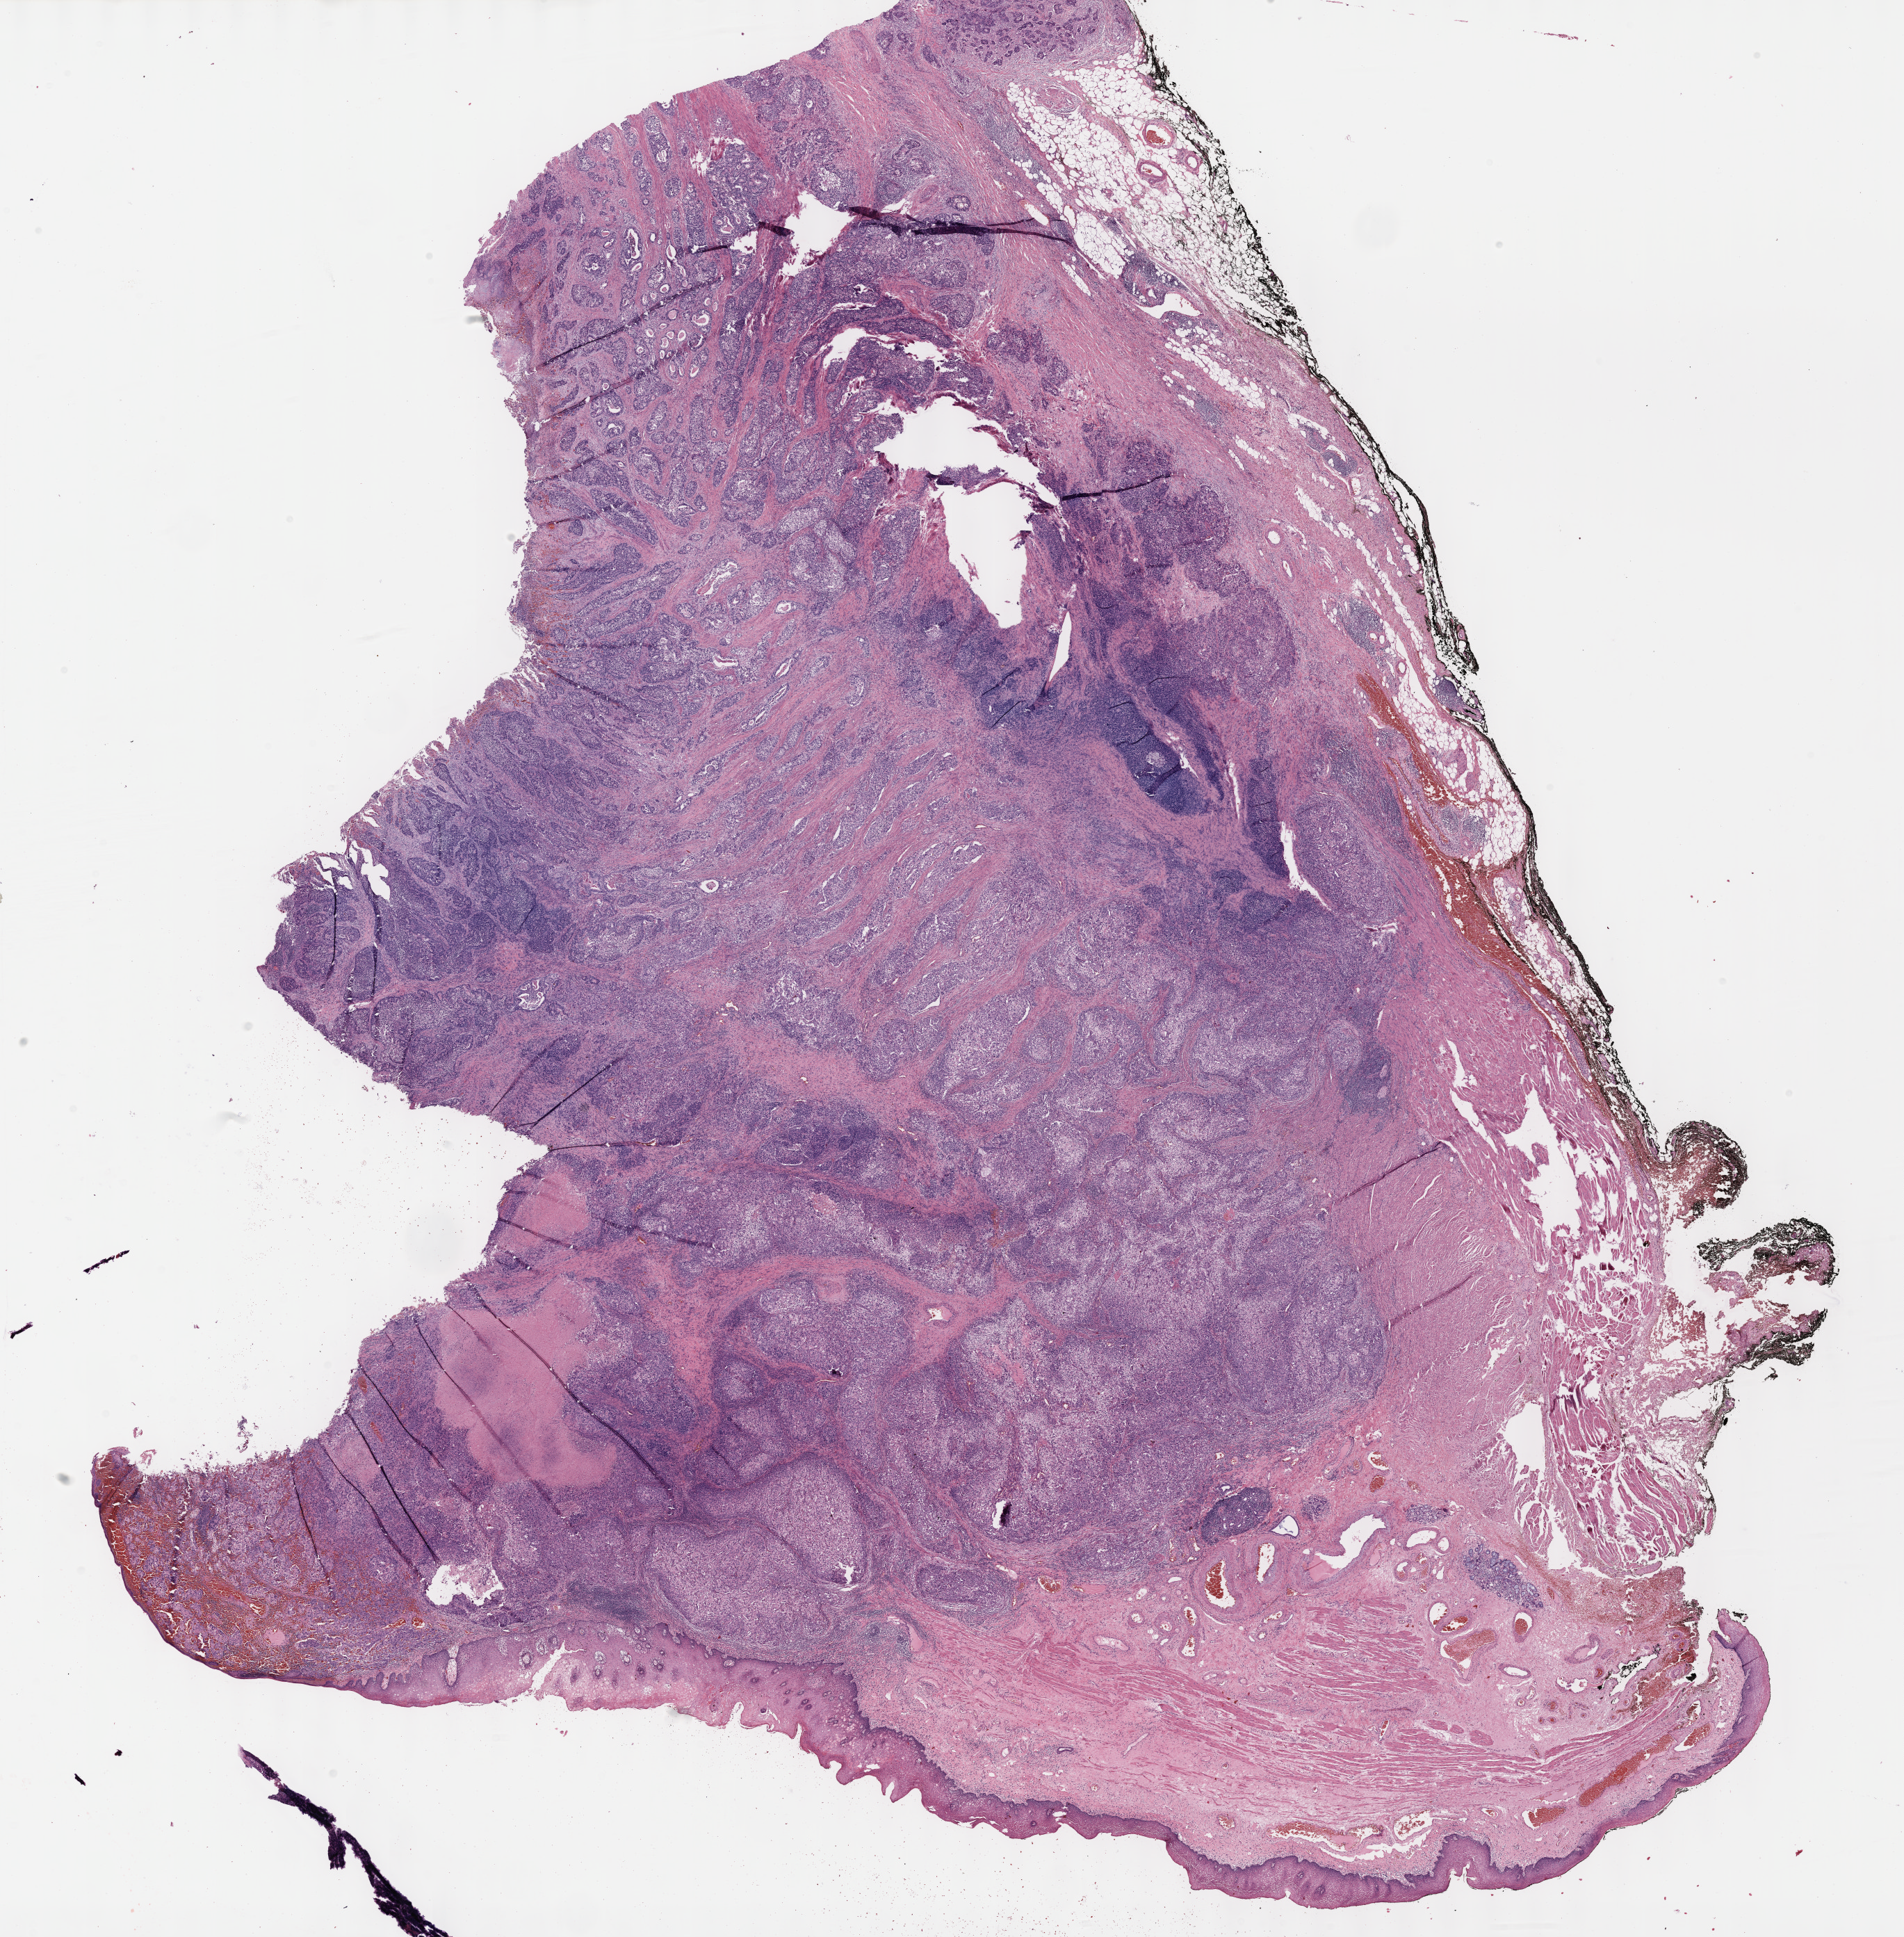
H&E whole-slide image, whole scanned area (about 22.1 x 22.5 mm, slide scanned at 40x) shown as a low-resolution overview; formalin-fixed paraffin-embedded (FFPE) diagnostic section; primary tumour sample from the stomach. Patient: male, age at initial diagnosis 75 years. Histologic grade: G3 (poorly differentiated).
- lymph nodes positive (case pathology): 3 of 27 examined
- histologic diagnosis: Adenocarcinoma, intestinal type (cardia, NOS)
- AJCC pathologic stage: IIIB (7th edition)